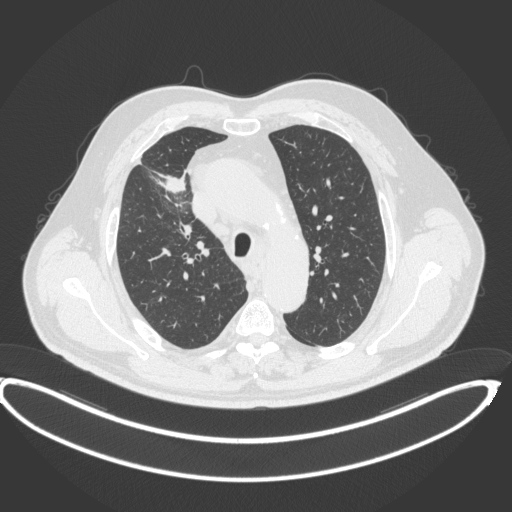
Chest CT, one axial slice. Position 300 of 395 along the scan axis. 120 kVp. Lung window (W 1500 / L -600 HU). 1 mm slice thickness. 512 × 512 image matrix. Male patient, age 62 years. Case-level facts recorded for this patient, not image findings: clinical TNM (as recorded): T1c N3 M1c.
Outlined on this slice (bounding box drawn by a radiologist):
- lung tumour (recorded histology: adenocarcinoma): bounding box <161,169,190,194> (left, top, right, bottom; pixels)